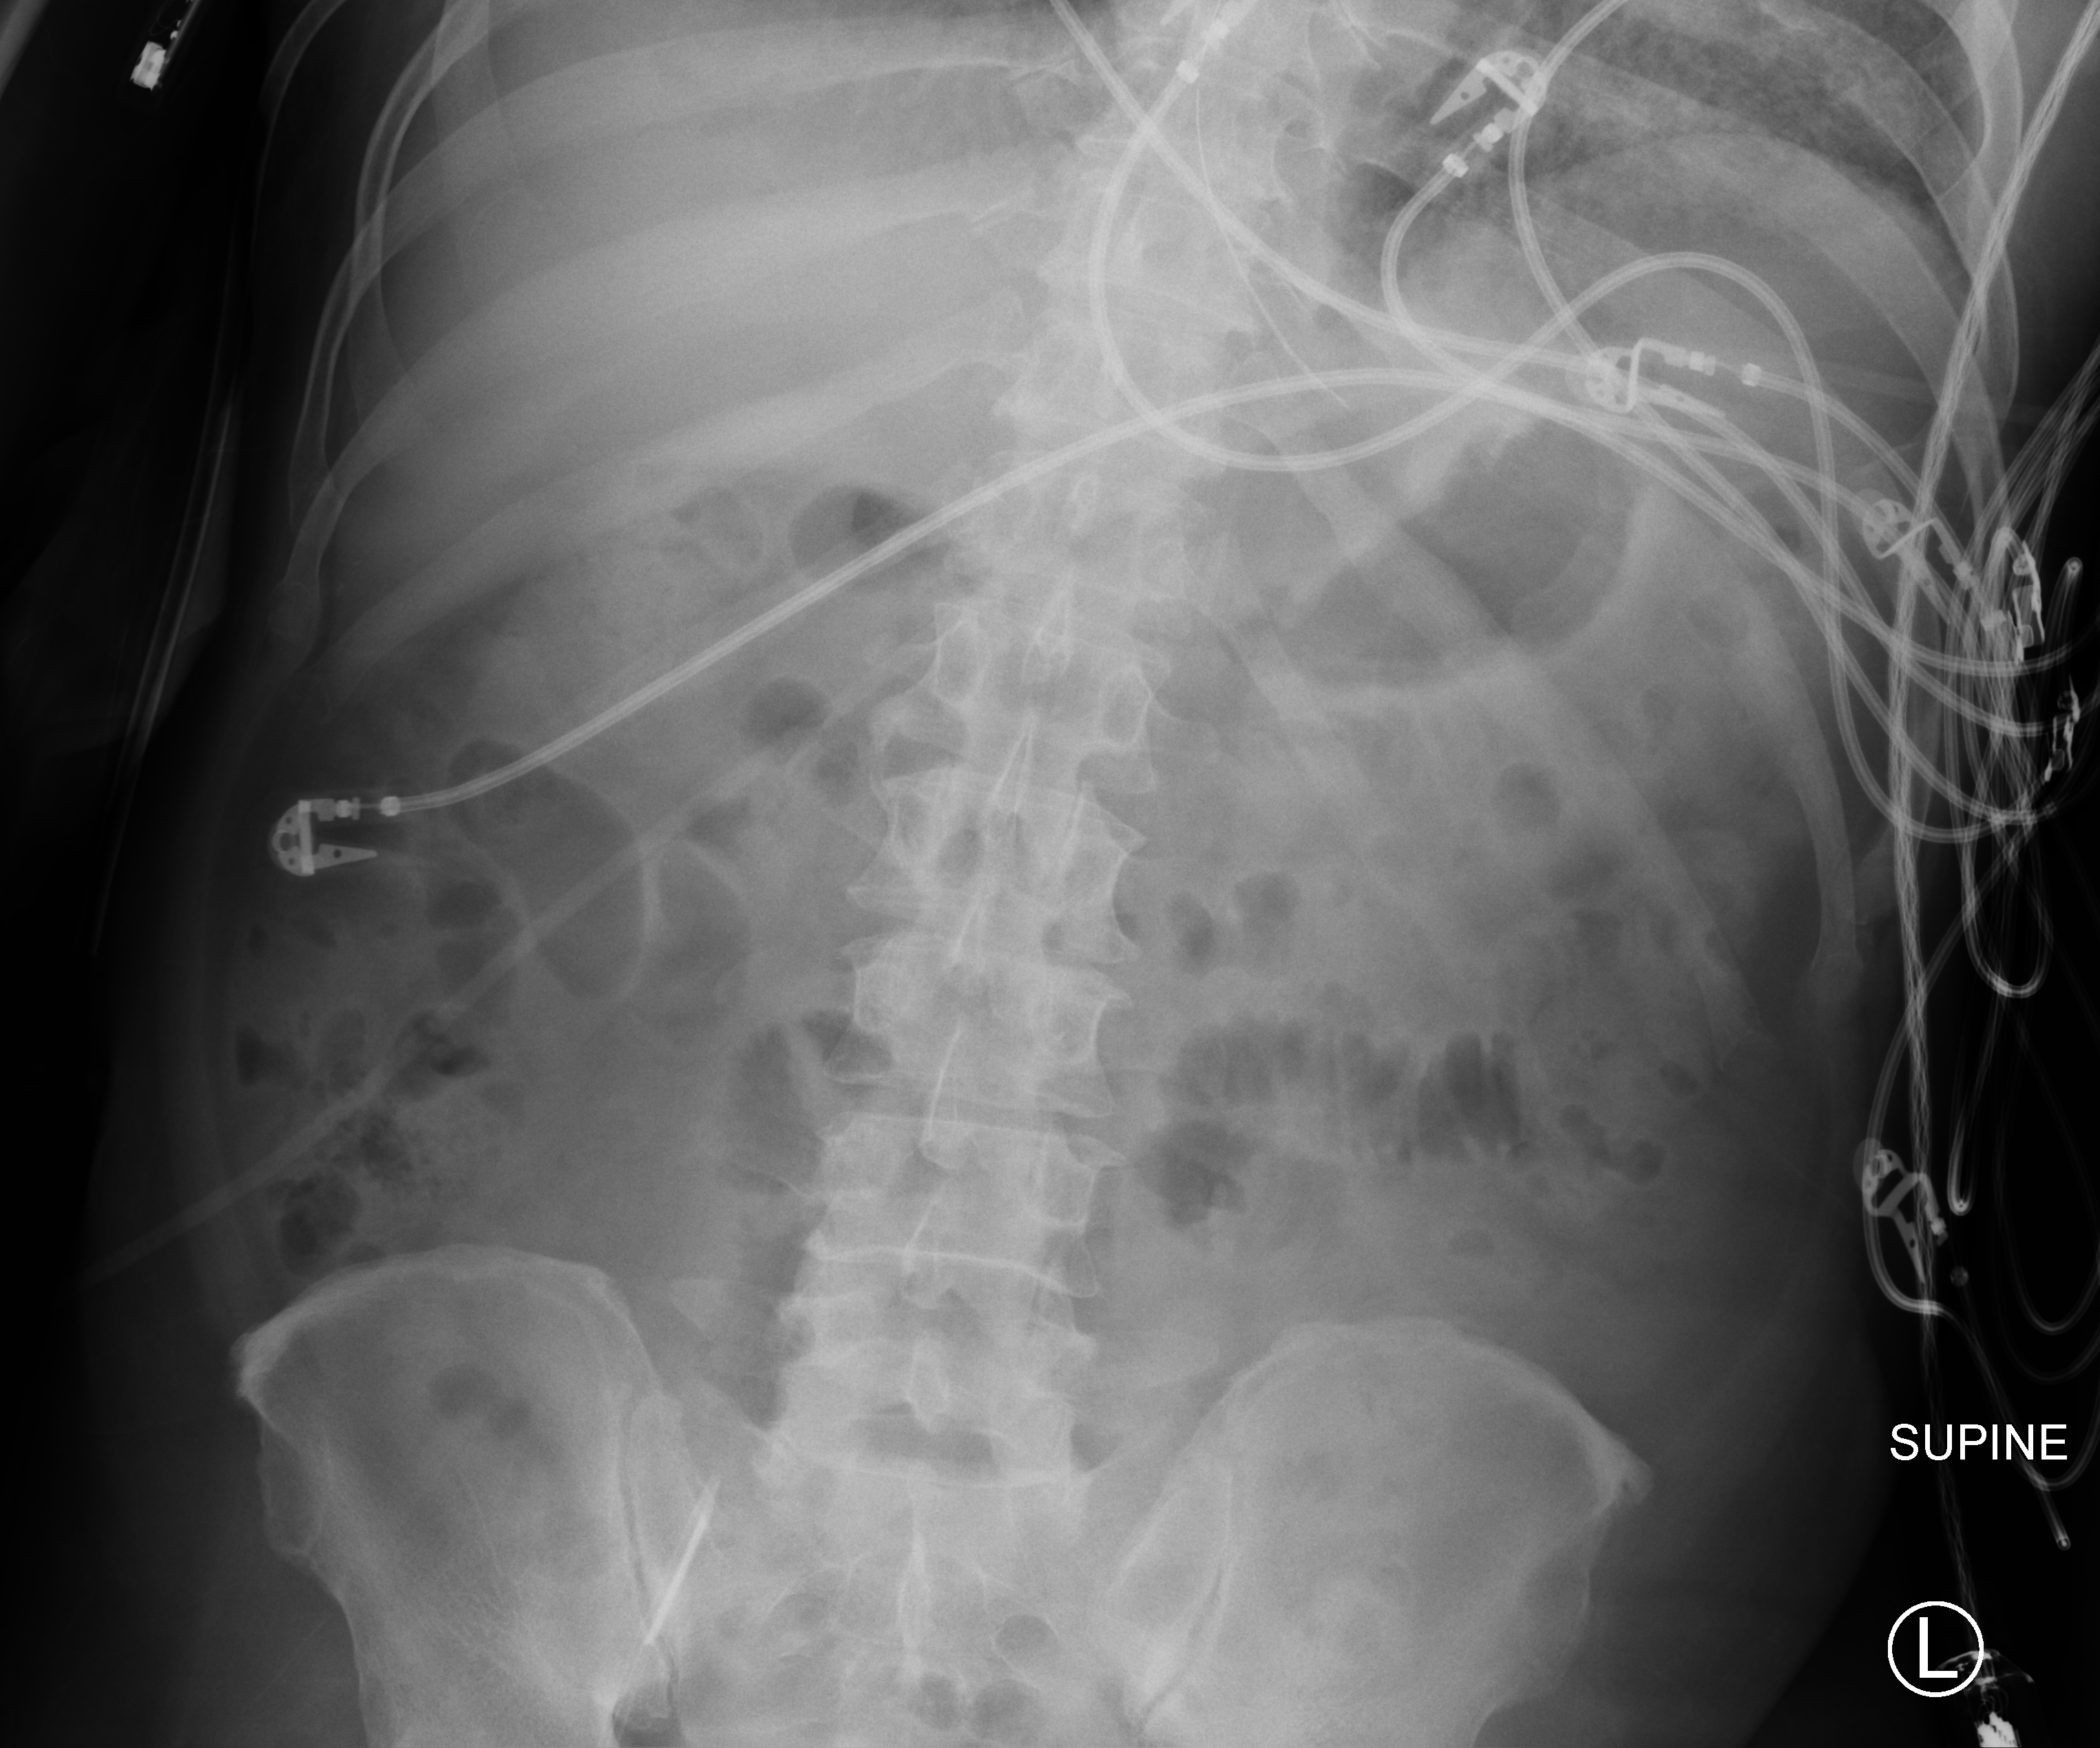
Portable abdomen radiograph; anteroposterior (AP) projection. Male patient hospitalised with COVID-19, age 18–59 years.
Admission-level facts for this patient (not findings on this image; timing relative to this image not recorded): length of hospital stay: 77 days; admitted to intensive care during this hospital stay: yes; mechanically ventilated during this hospital stay: yes.